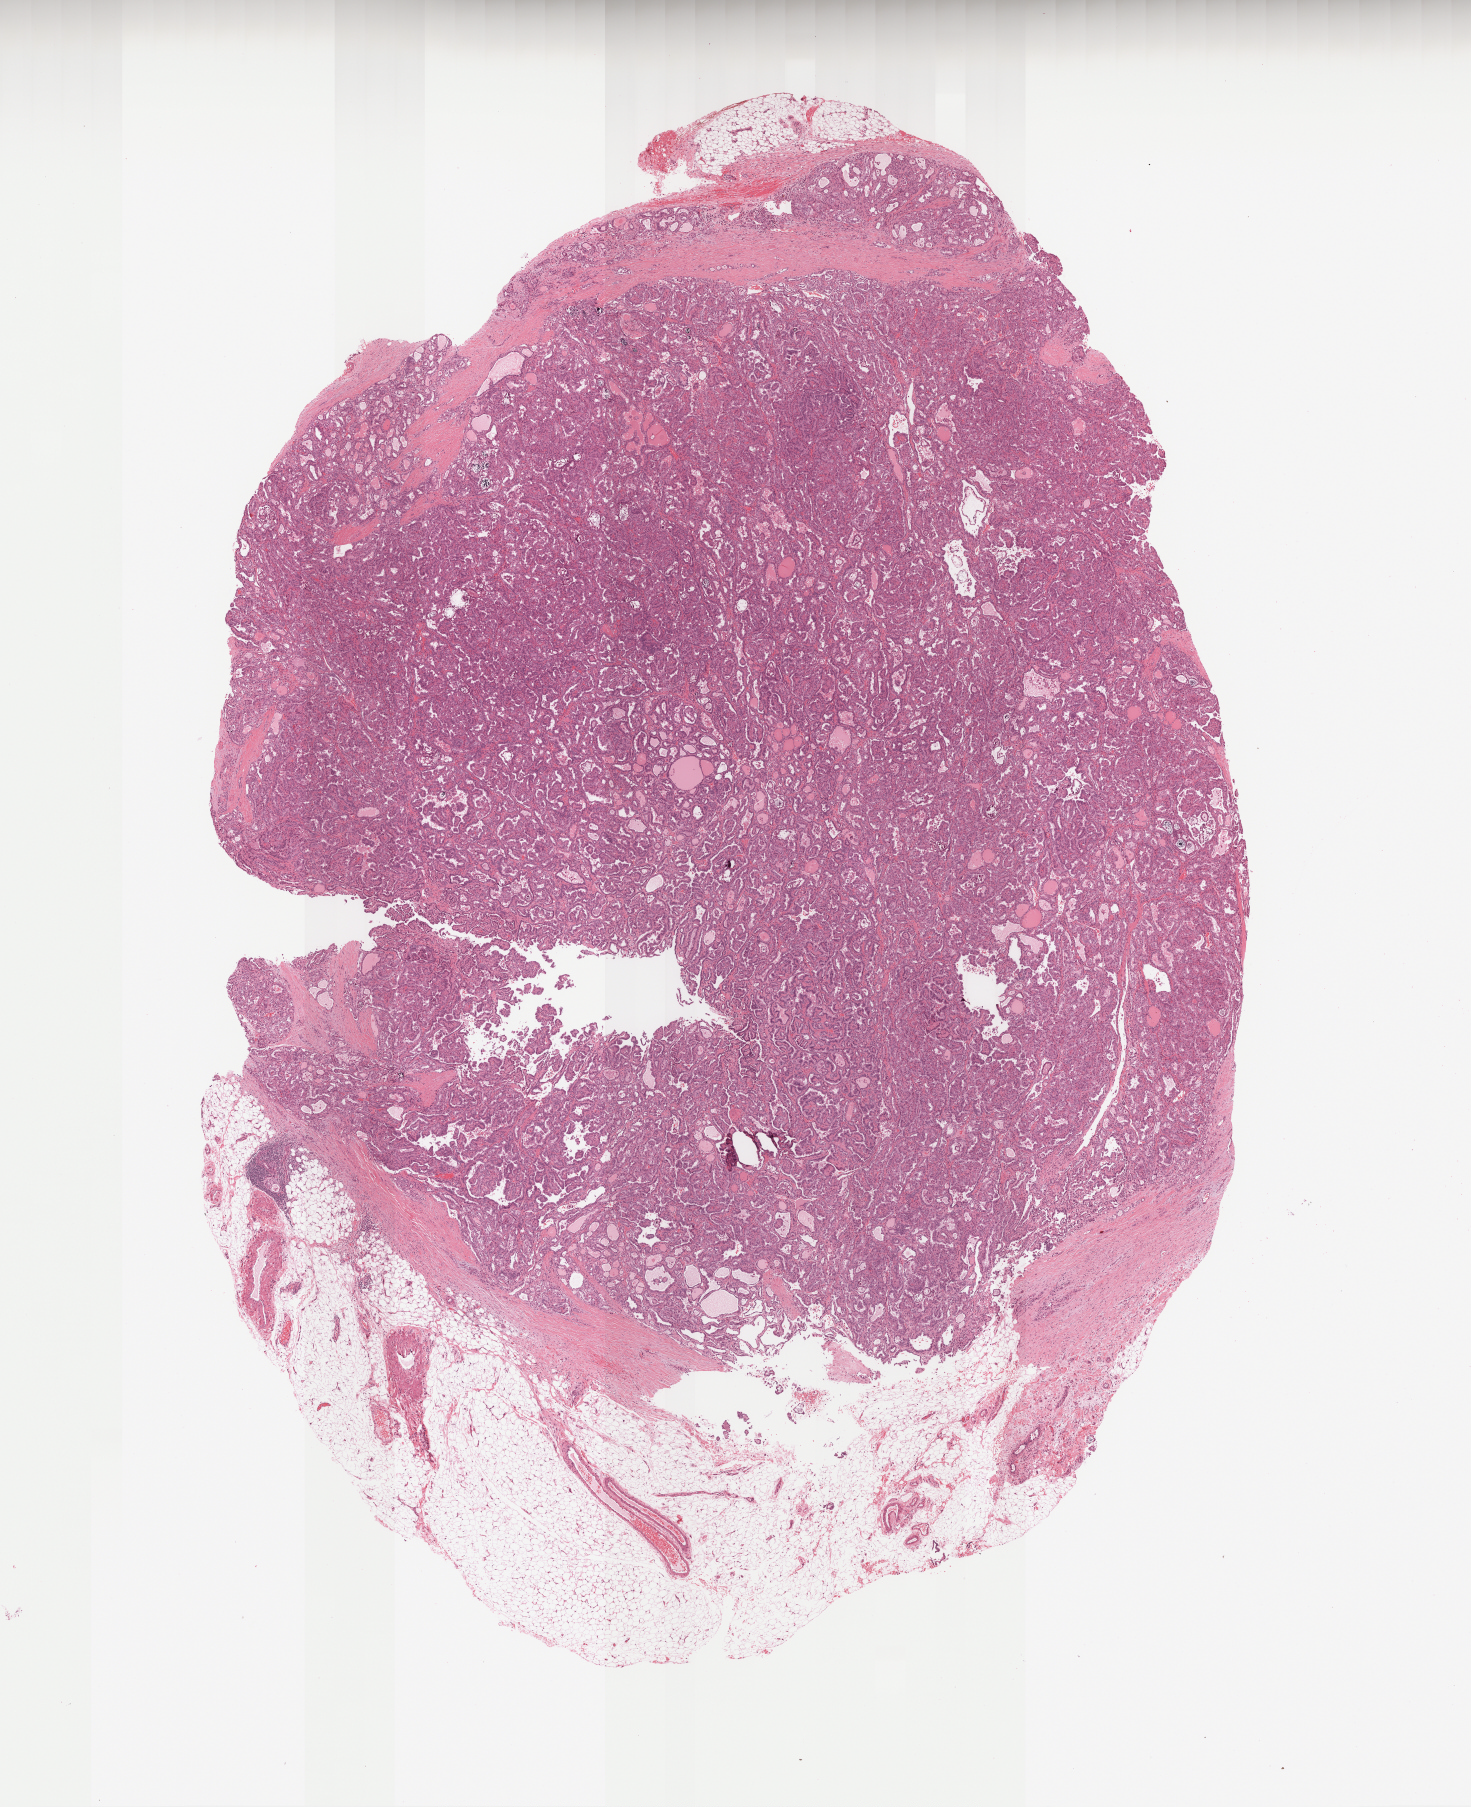
Whole-slide histology image, H&E-stained, whole scanned area (about 11.9 x 14.6 mm) shown as a low-resolution overview, formalin-fixed paraffin-embedded (FFPE) diagnostic section, primary tumour sample from the thyroid. Female patient; age at initial diagnosis 51 years.
AJCC pathologic stage: IVA. Pathologic diagnosis: Papillary carcinoma, oxyphilic cell (thyroid gland). Laterality: right. Lymph nodes positive (case pathology): 35 of 49 examined.